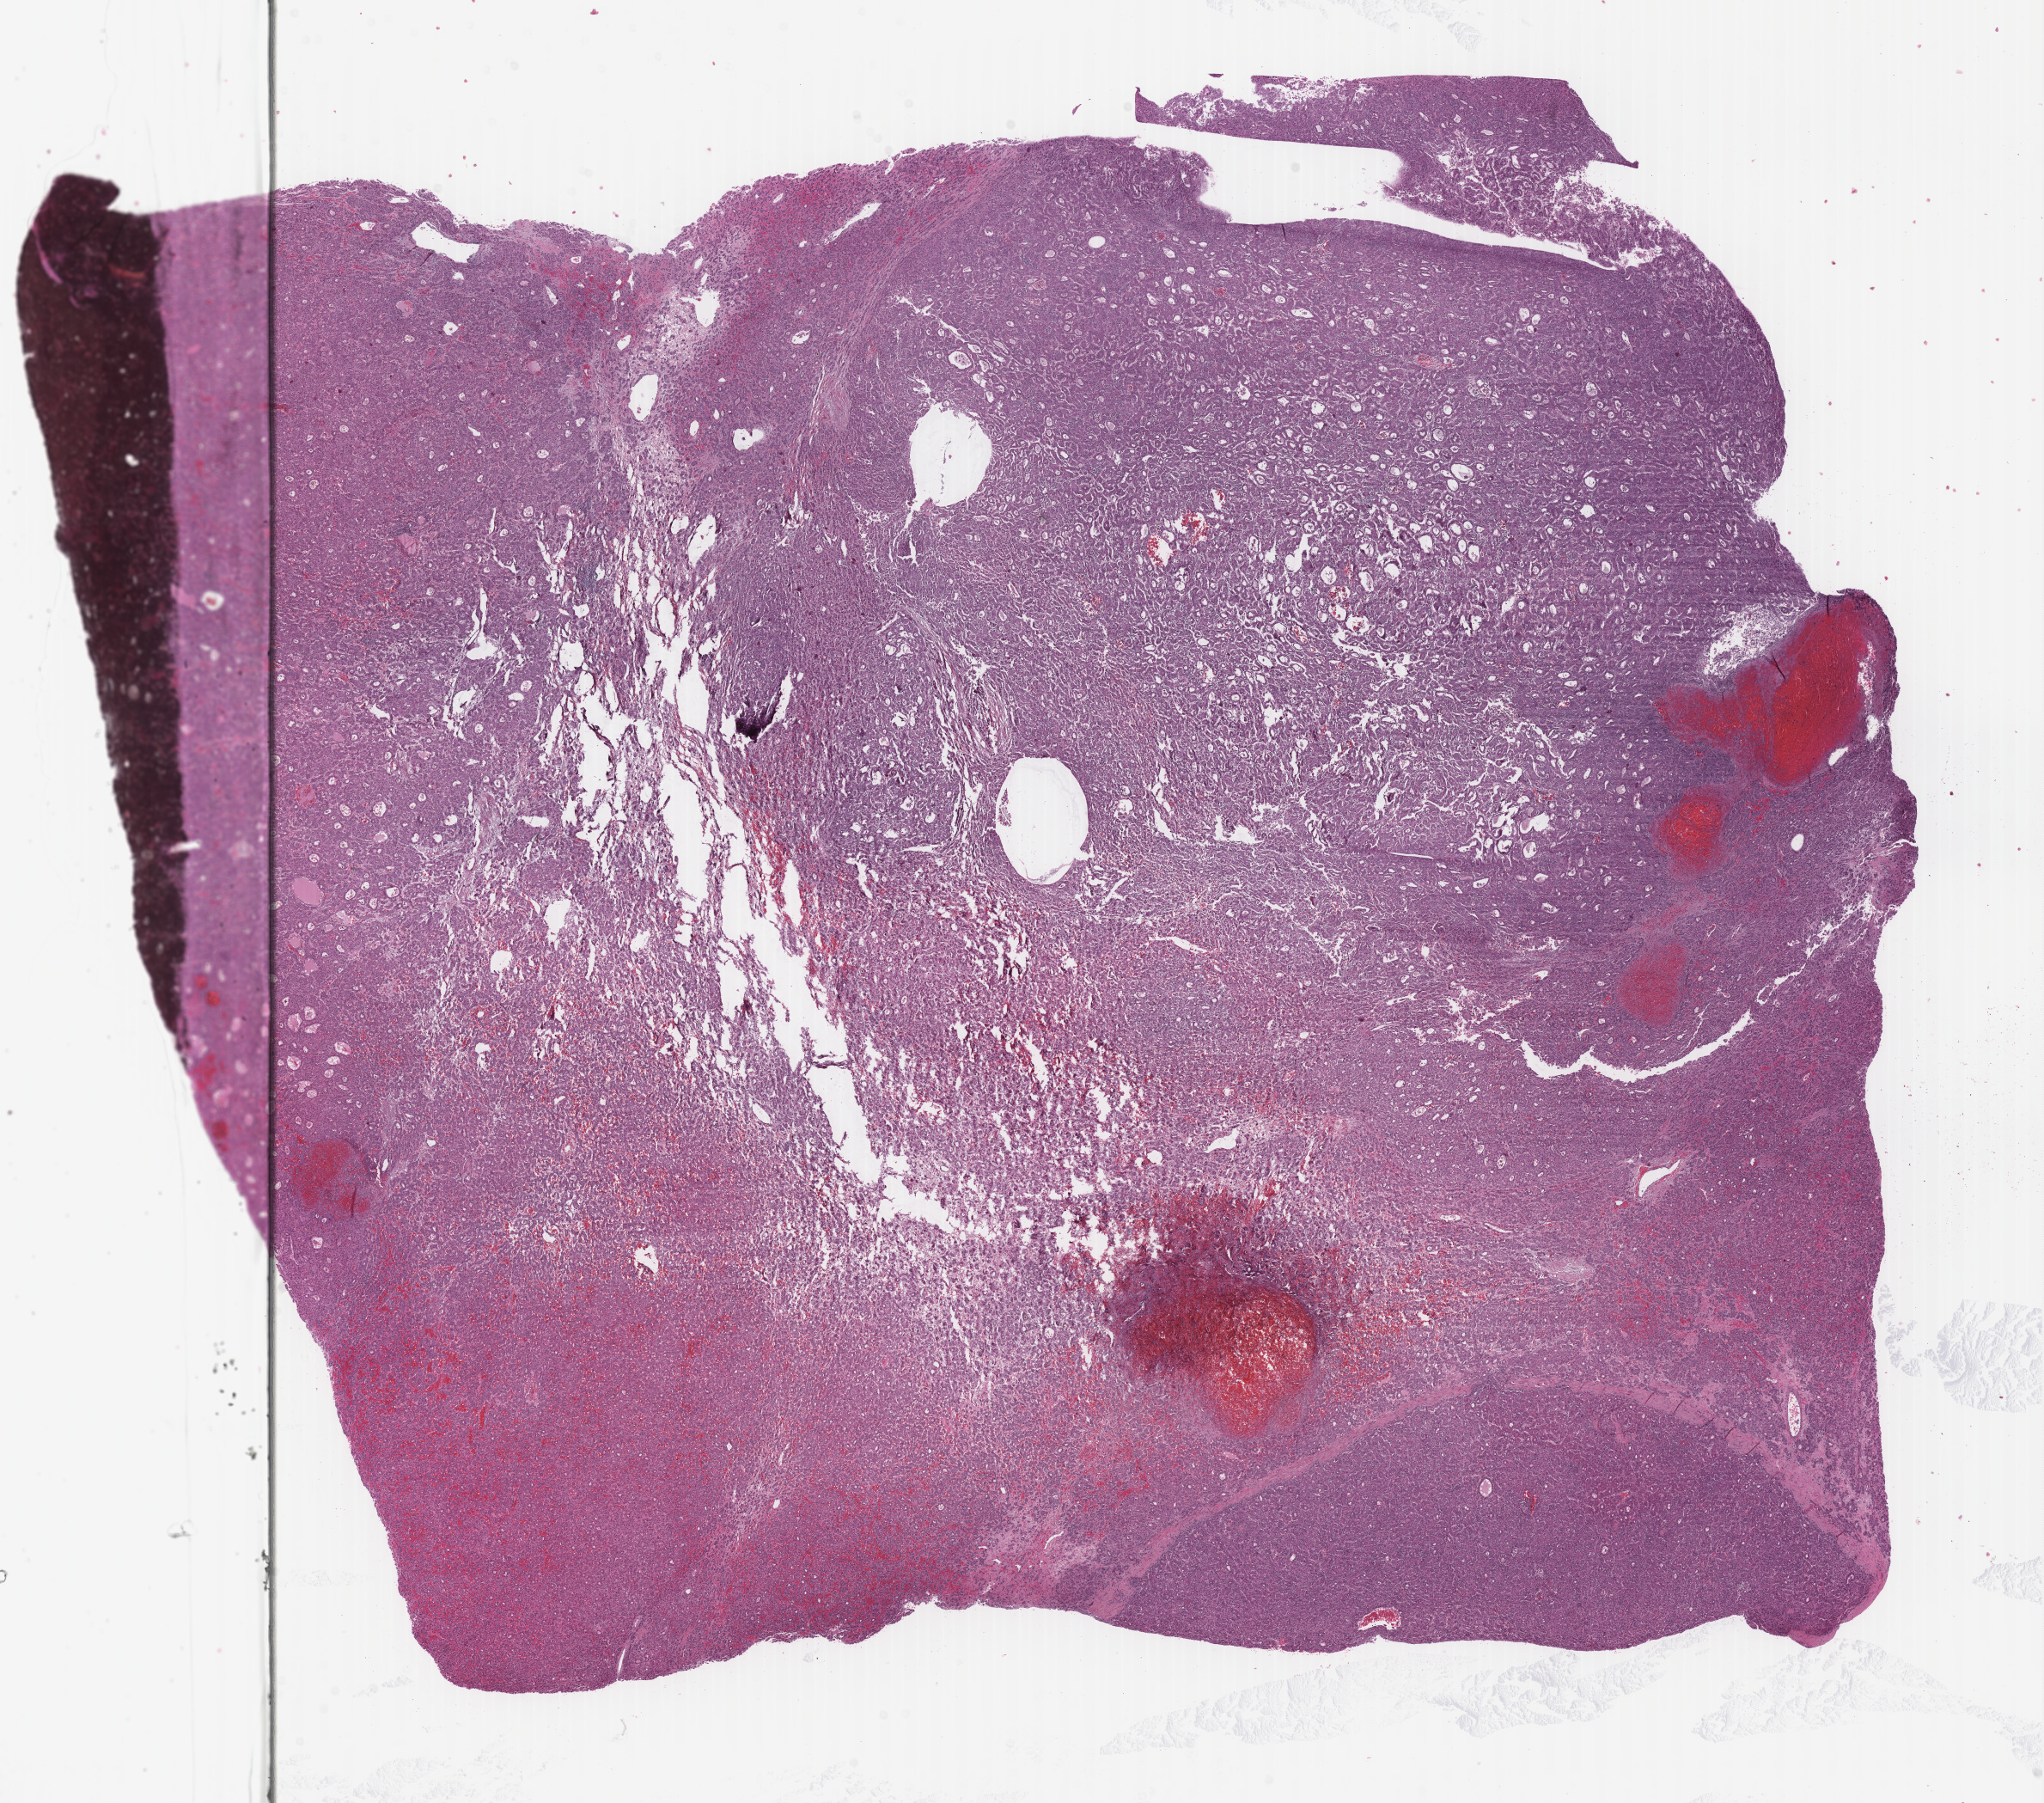
H&E whole-slide image — whole scanned area (about 18.8 x 16.6 mm) shown as a low-resolution overview, formalin-fixed paraffin-embedded (FFPE) diagnostic section, sample: primary tumour, liver. Male, age 69 years at initial diagnosis. Histologic grade: G1 (well differentiated).
• AJCC pathologic stage: I (7th edition)
• diagnosis: Hepatocellular carcinoma, NOS
• TNM: T1 N0 M0